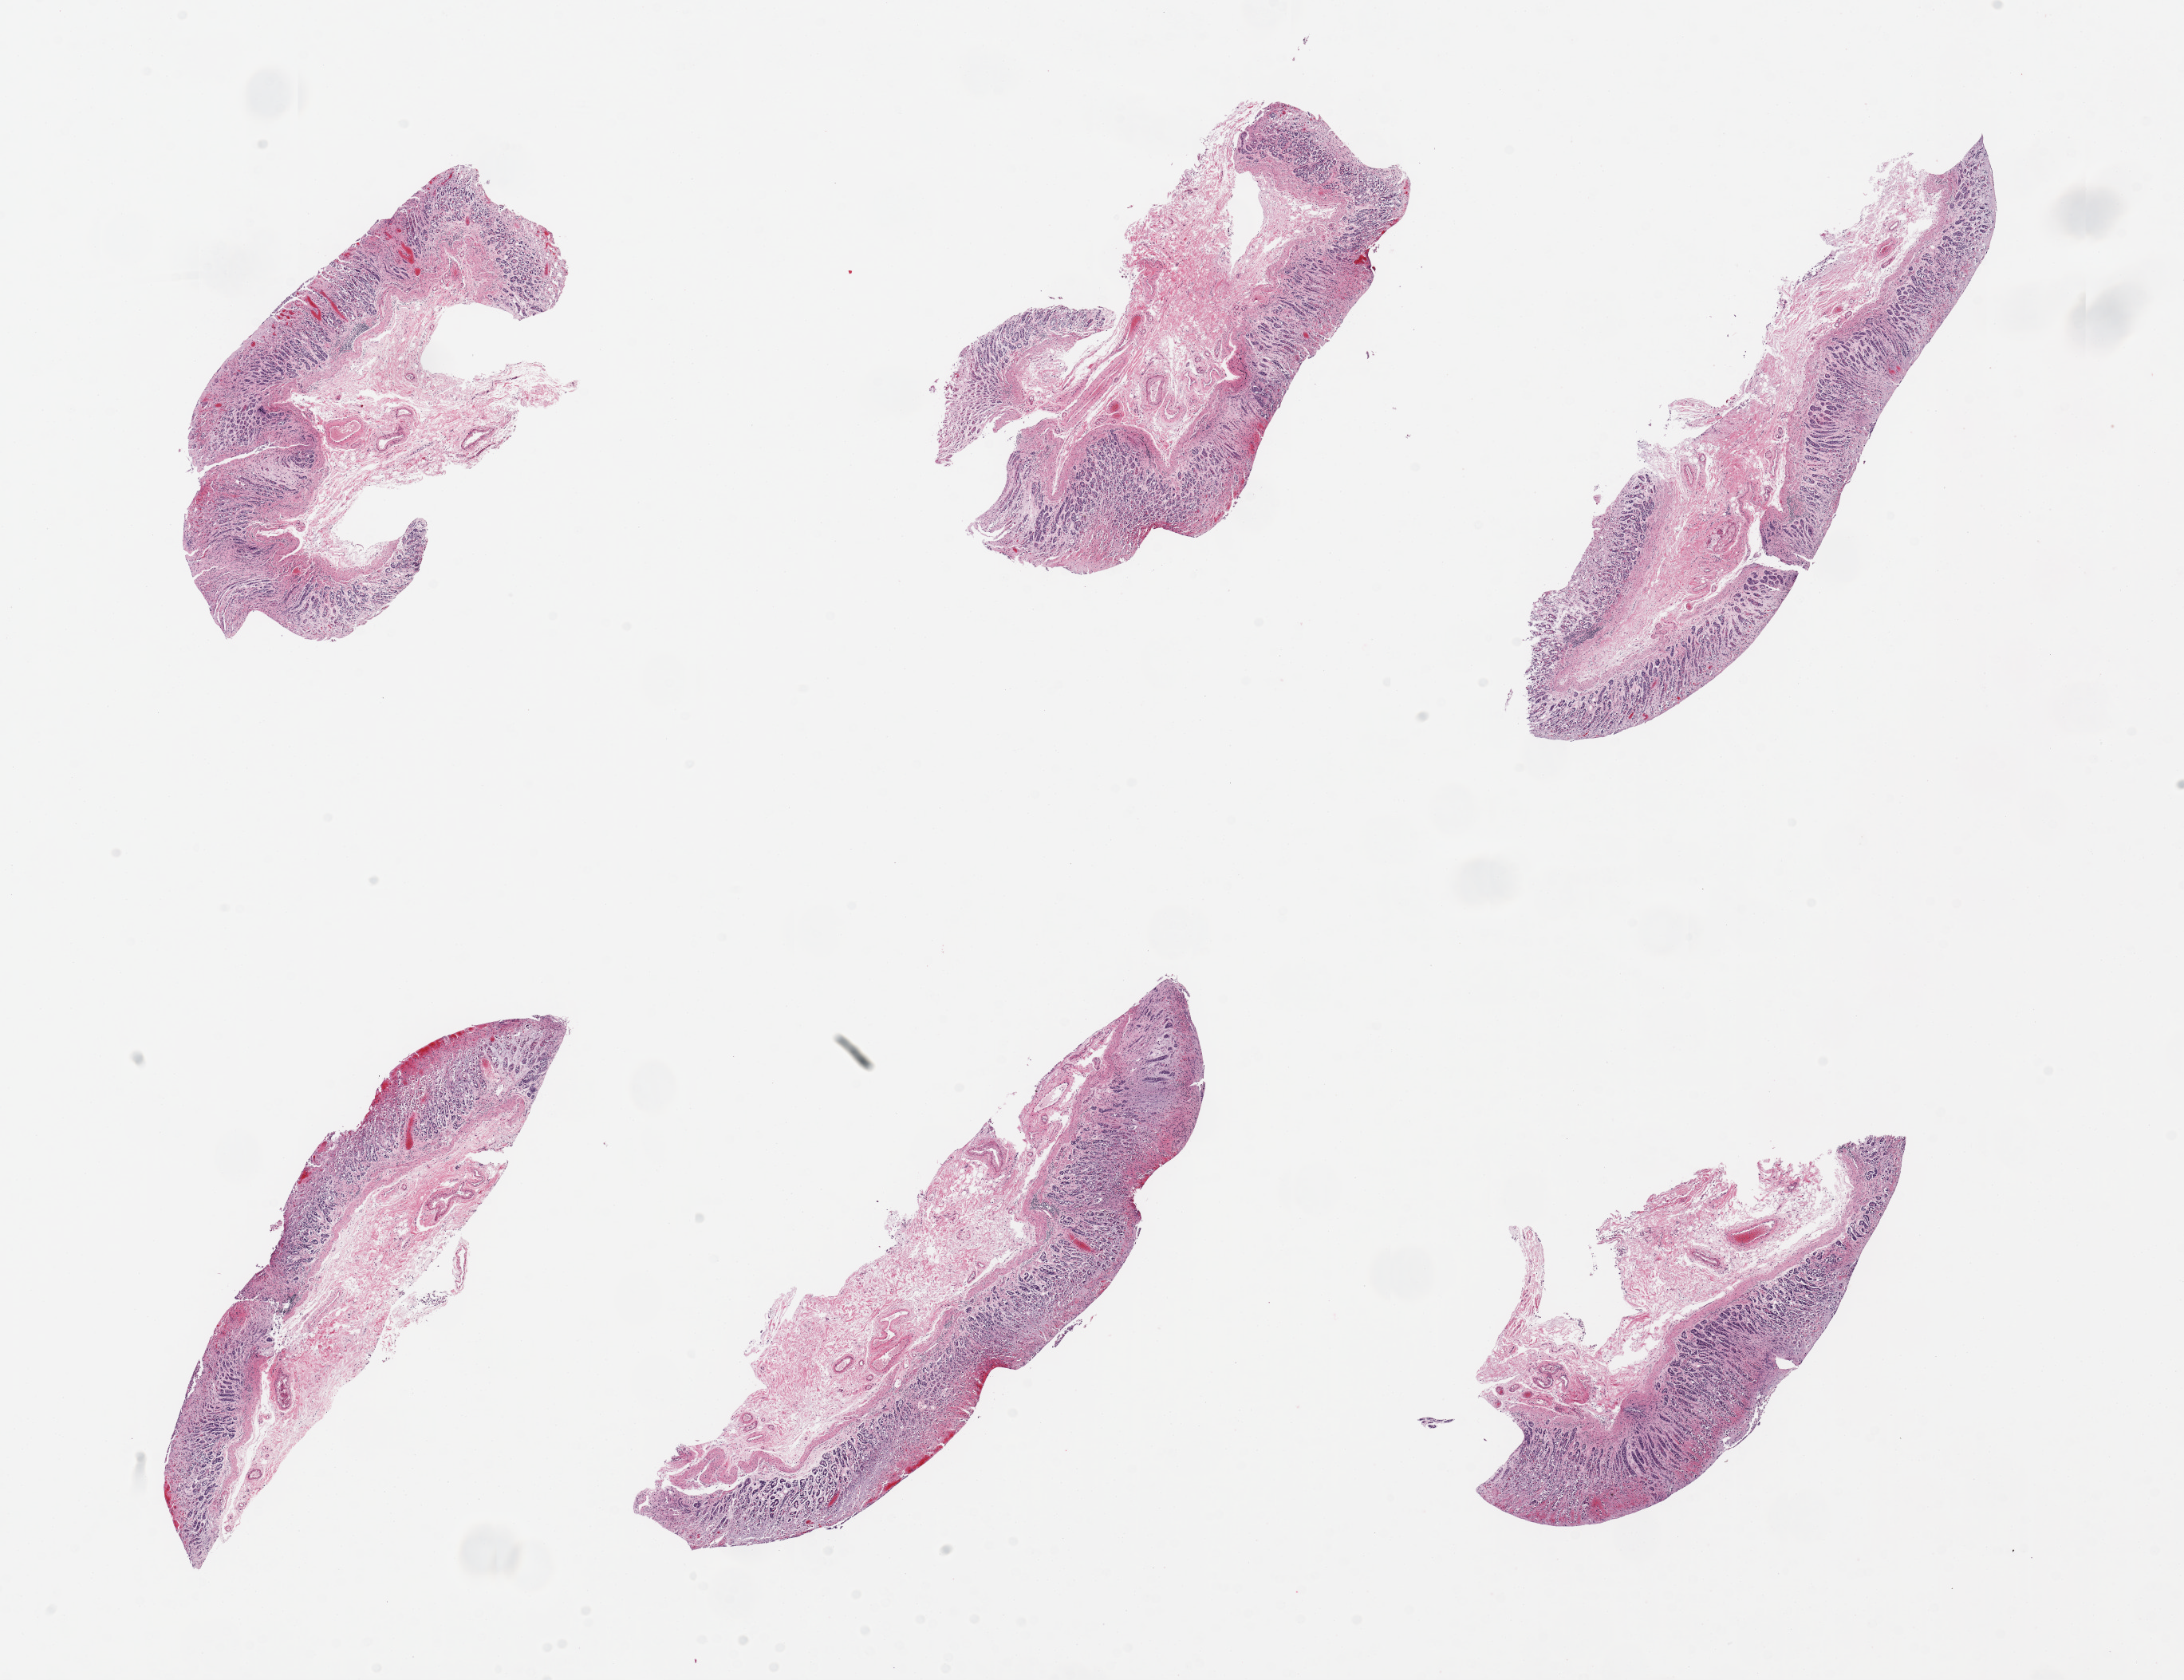
Whole-slide image, hematoxylin and eosin (H&E) stain, low-resolution overview of the scanned area, about 21.7 x 16.7 mm (slide scanned at 20x), PAXgene-fixed paraffin-embedded (PFPE) section, target tissue: stomach, donor tissue sample. Female donor.
Reviewer comment on this tissue sample: 6 pieces, mucosa up to ~0.8mm but with advanced autolysis.